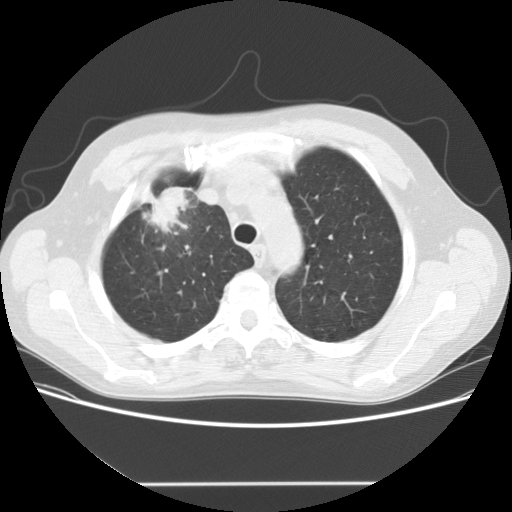
Low-dose screening chest CT, one axial slice; position 123 of 153 along the scan axis; 120 kVp; lung window (W 1500 / L -600 HU); 2.5 mm slice thickness; 512 × 512 image matrix, field of view 360 × 360 mm.
Annotated regions visible in this slice (expert manual segmentation):
- lesion 1 (tumor, upper lobe of right lung): bounding box [x1, y1, x2, y2] px = [142, 187, 191, 233]